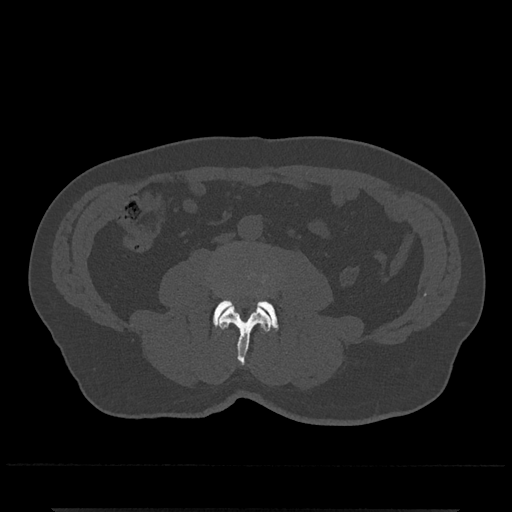
CT including the spine, one axial slice. Position 194 of 797 along the scan axis. Reconstruction kernel Br40s/3. 120 kVp. Bone window (W 1800 / L 400 HU). 512 × 512 image matrix, field of view 393 × 393 mm. Patient: male, 67 years. Case-level facts recorded for this patient, not image findings: primary cancer: prostate.
Outlined on this slice (semi-automatically segmented with operator editing):
- L3 vertebra: box from (x=218, y=277) to (x=272, y=365) px
- L4 vertebra: (x=213, y=299)–(x=278, y=330)